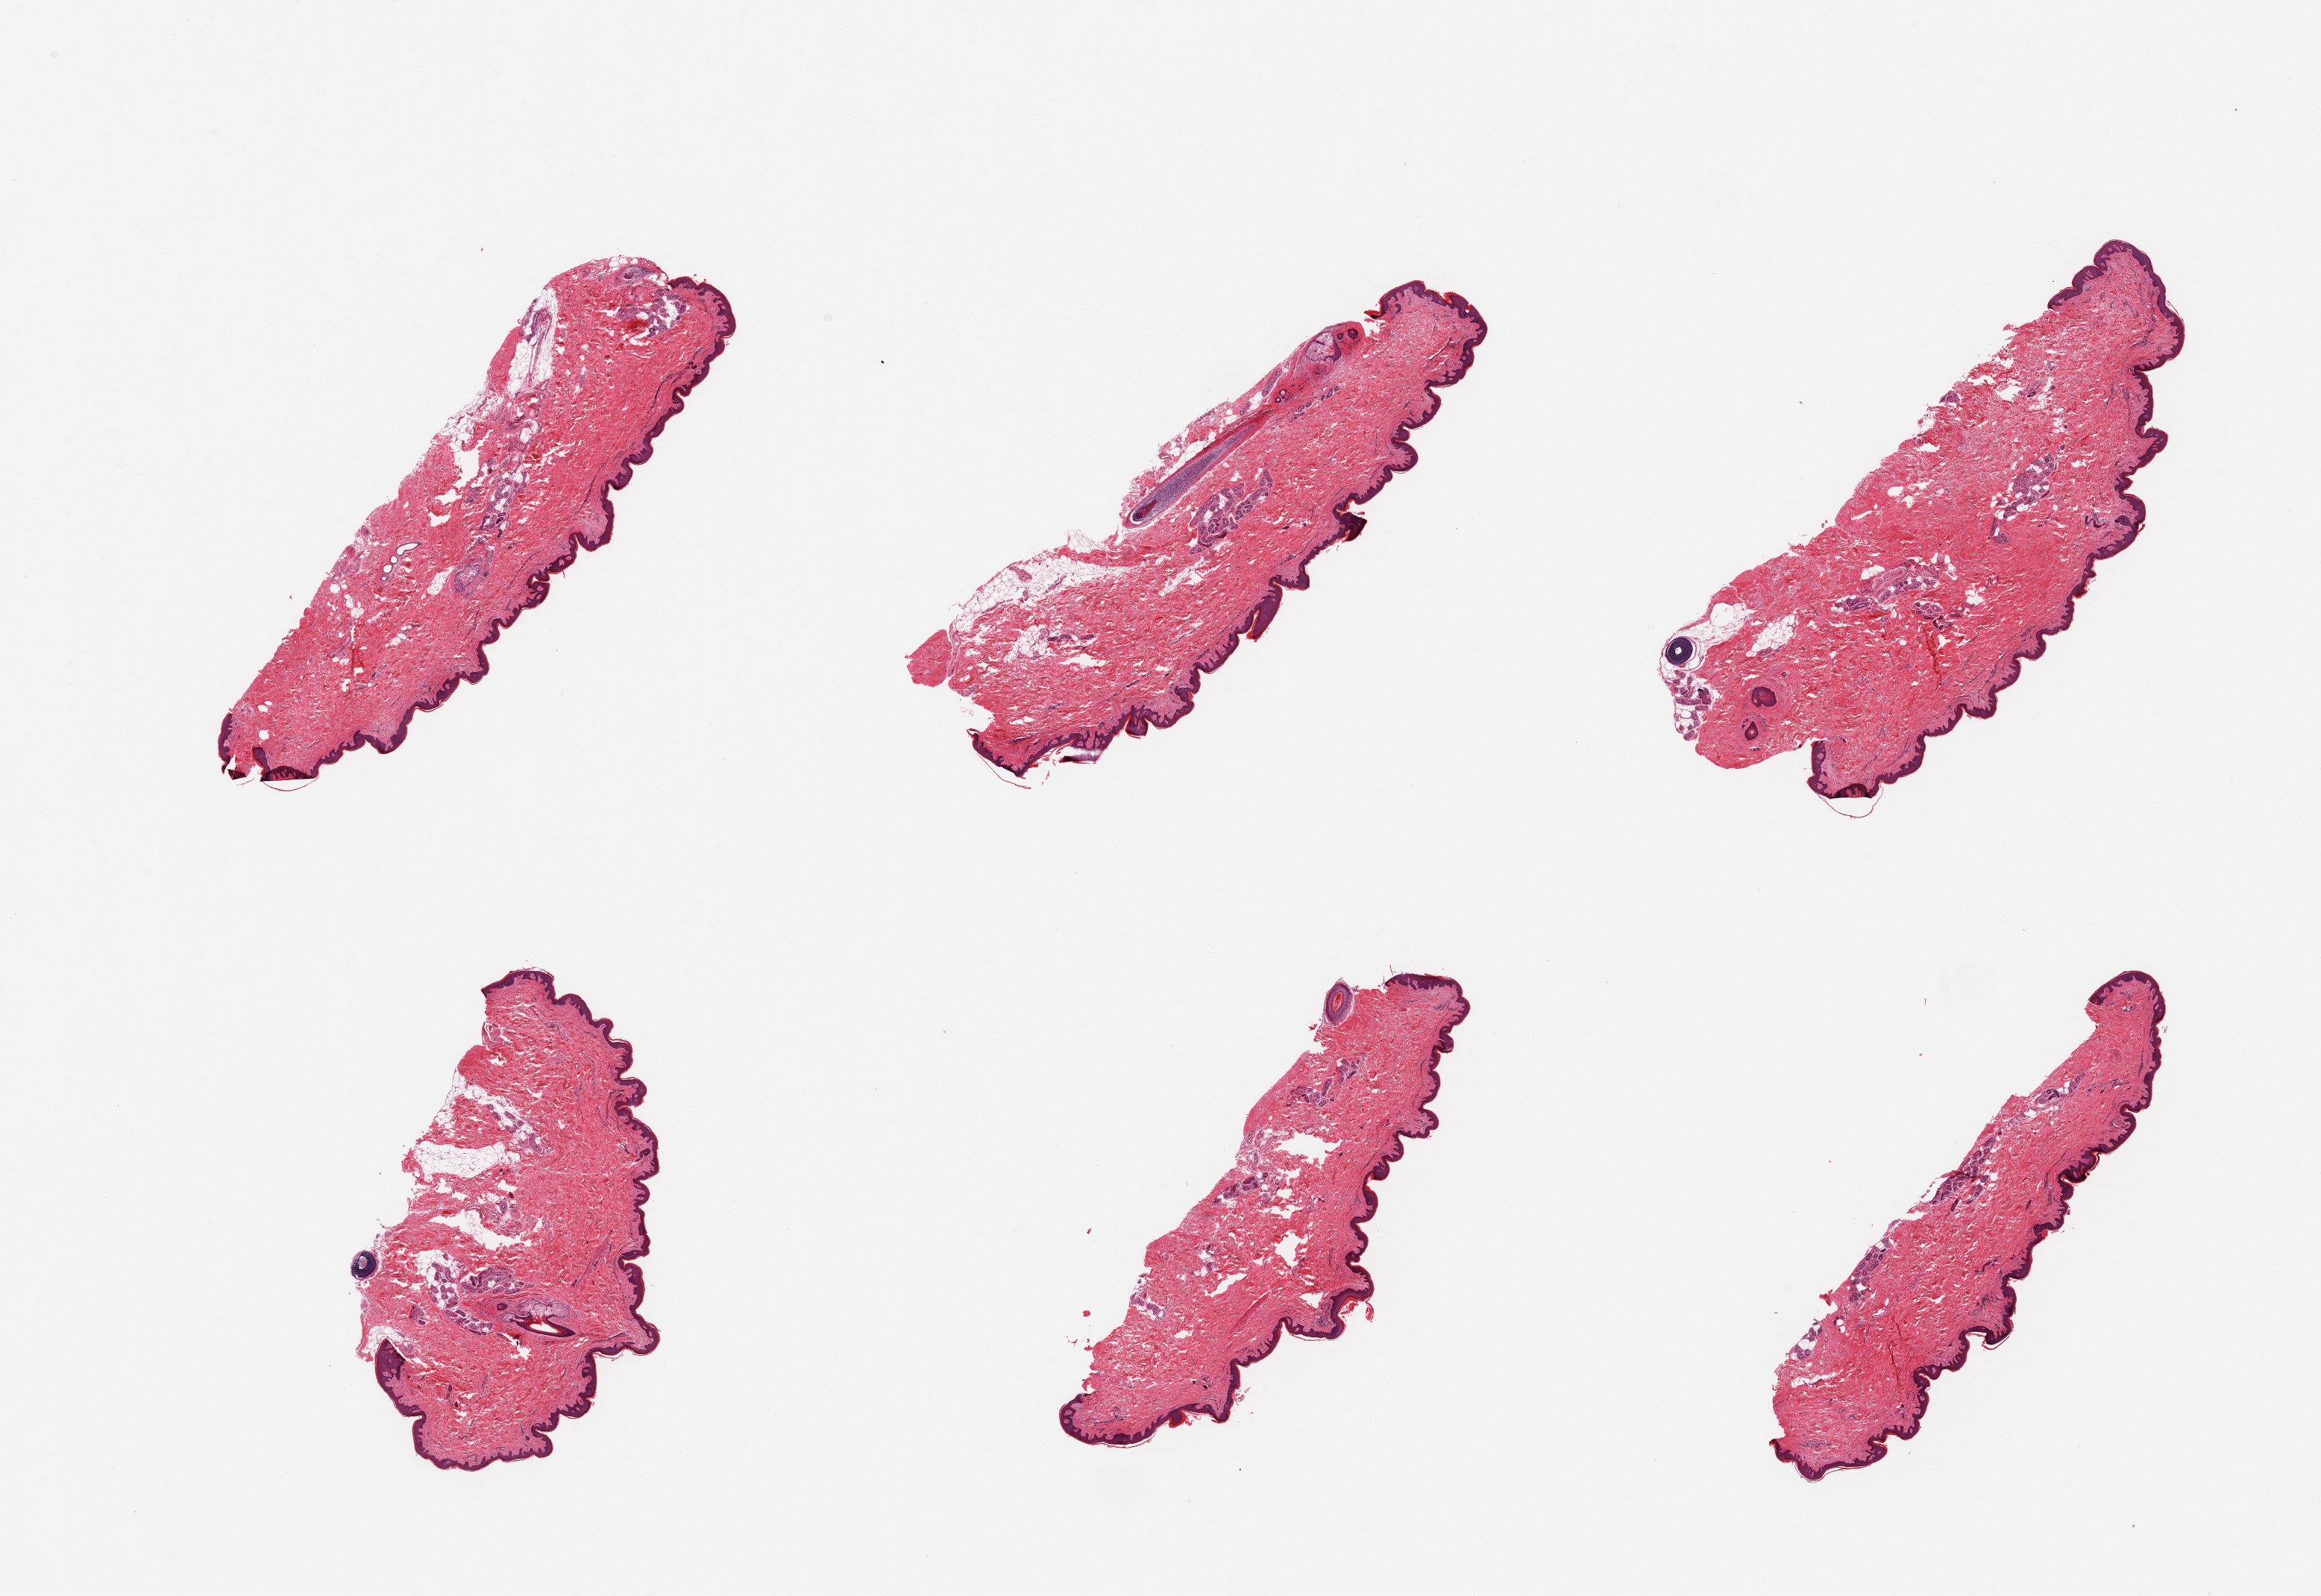
Whole-slide image, haematoxylin and eosin stain — shown as a low-resolution overview of the whole scanned area (about 24.6 x 16.9 mm, acquisition: 20x scan). PAXgene-fixed paraffin-embedded (PFPE) section. Section of skin of suprapubic region (target tissue). Tissue donor sample. Donor: male.
Reviewer comment on this tissue sample: 6 pieces; relatively well trimmed, 5-10% fat.